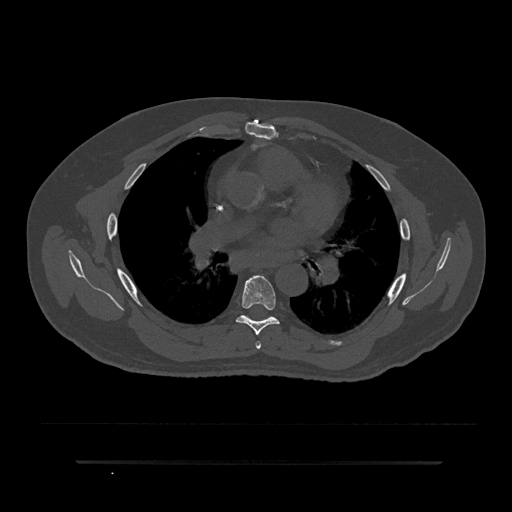
CT including the spine, one axial slice. Position 525 of 797 along the scan axis. 120 kVp. Bone window (W 1800 / L 400 HU). 0.5 mm slice thickness. 512 × 512 image matrix, field of view 464 × 464 mm. Patient: male, 59 years. Case-level facts recorded for this patient, not image findings: primary cancer: bile ducts; vertebrae with lytic lesions (as recorded): T10.
Annotated regions visible in this slice (semi-automatically segmented with operator editing):
- T5 vertebra: box from (x=255, y=341) to (x=261, y=349) px
- T6 vertebra: (x=235, y=275)–(x=280, y=335)